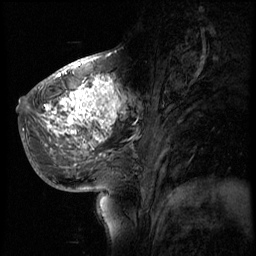
Breast MRI (dynamic contrast-enhanced), one sagittal slice. Slice 26 of 56 in the series (ordered by position). 4 images stored at this slice position (order not interpretable as contrast timing). 1.5 T. TE 4.2 ms, TR 8.9 ms. 2.5 mm slice thickness. 256 × 256 image matrix, field of view 220 × 220 mm. Patient: female, 51 years. Case-level facts recorded for this patient, not image findings: setting: breast cancer imaged before/during neoadjuvant chemotherapy; receptor status: triple-negative.
Annotated regions visible in this slice (semi-automatic segmentation, software-assisted and operator-edited):
- analysis volume of interest (the breast-tissue region the enhancement analysis was run in; not a lesion): bounding box (x1, y1, x2, y2) in pixels: (30, 70, 150, 173)
- tumour enhancement mask (voxels above the 140 % enhancement threshold inside the analysis volume of interest): (38, 74, 123, 147)